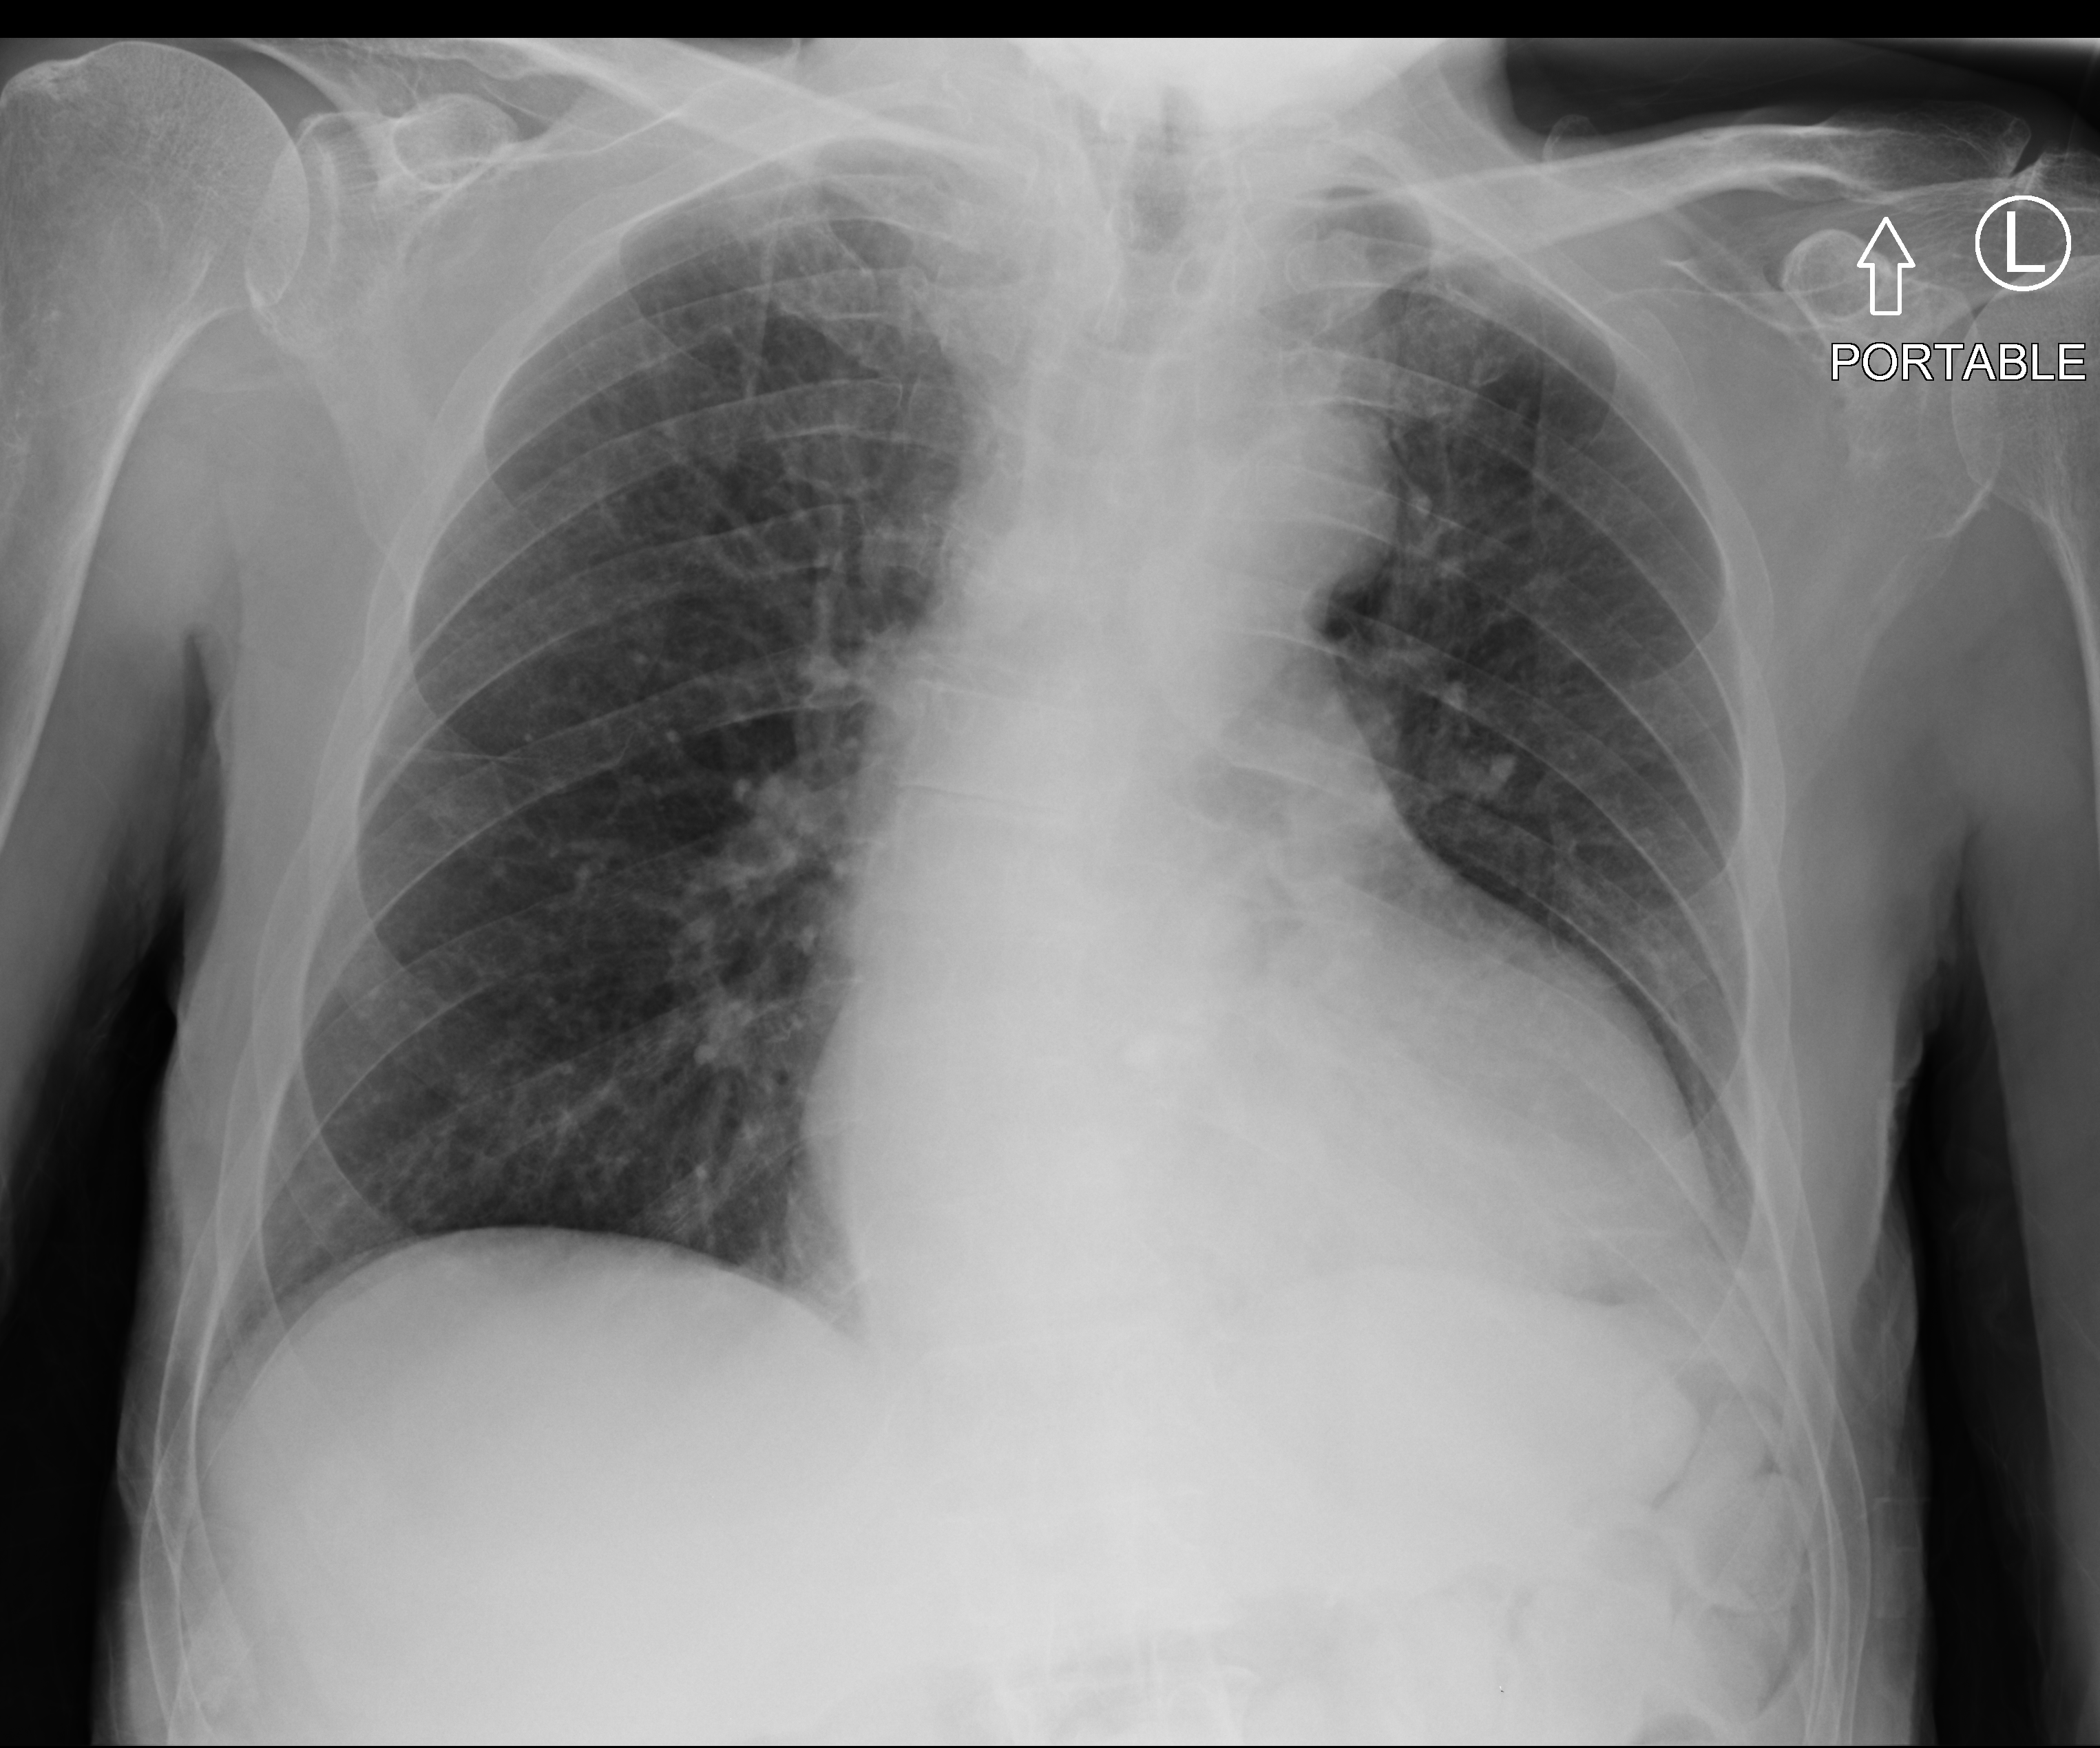
Portable chest radiograph. Male patient hospitalised with COVID-19, age 75–90 years.
Hospital-stay facts (about this admission, not read from this image; timing relative to this image not recorded):
- other chronic lung disease (admission record): no
- COPD (admission record): no
- mechanically ventilated during this hospital stay: no